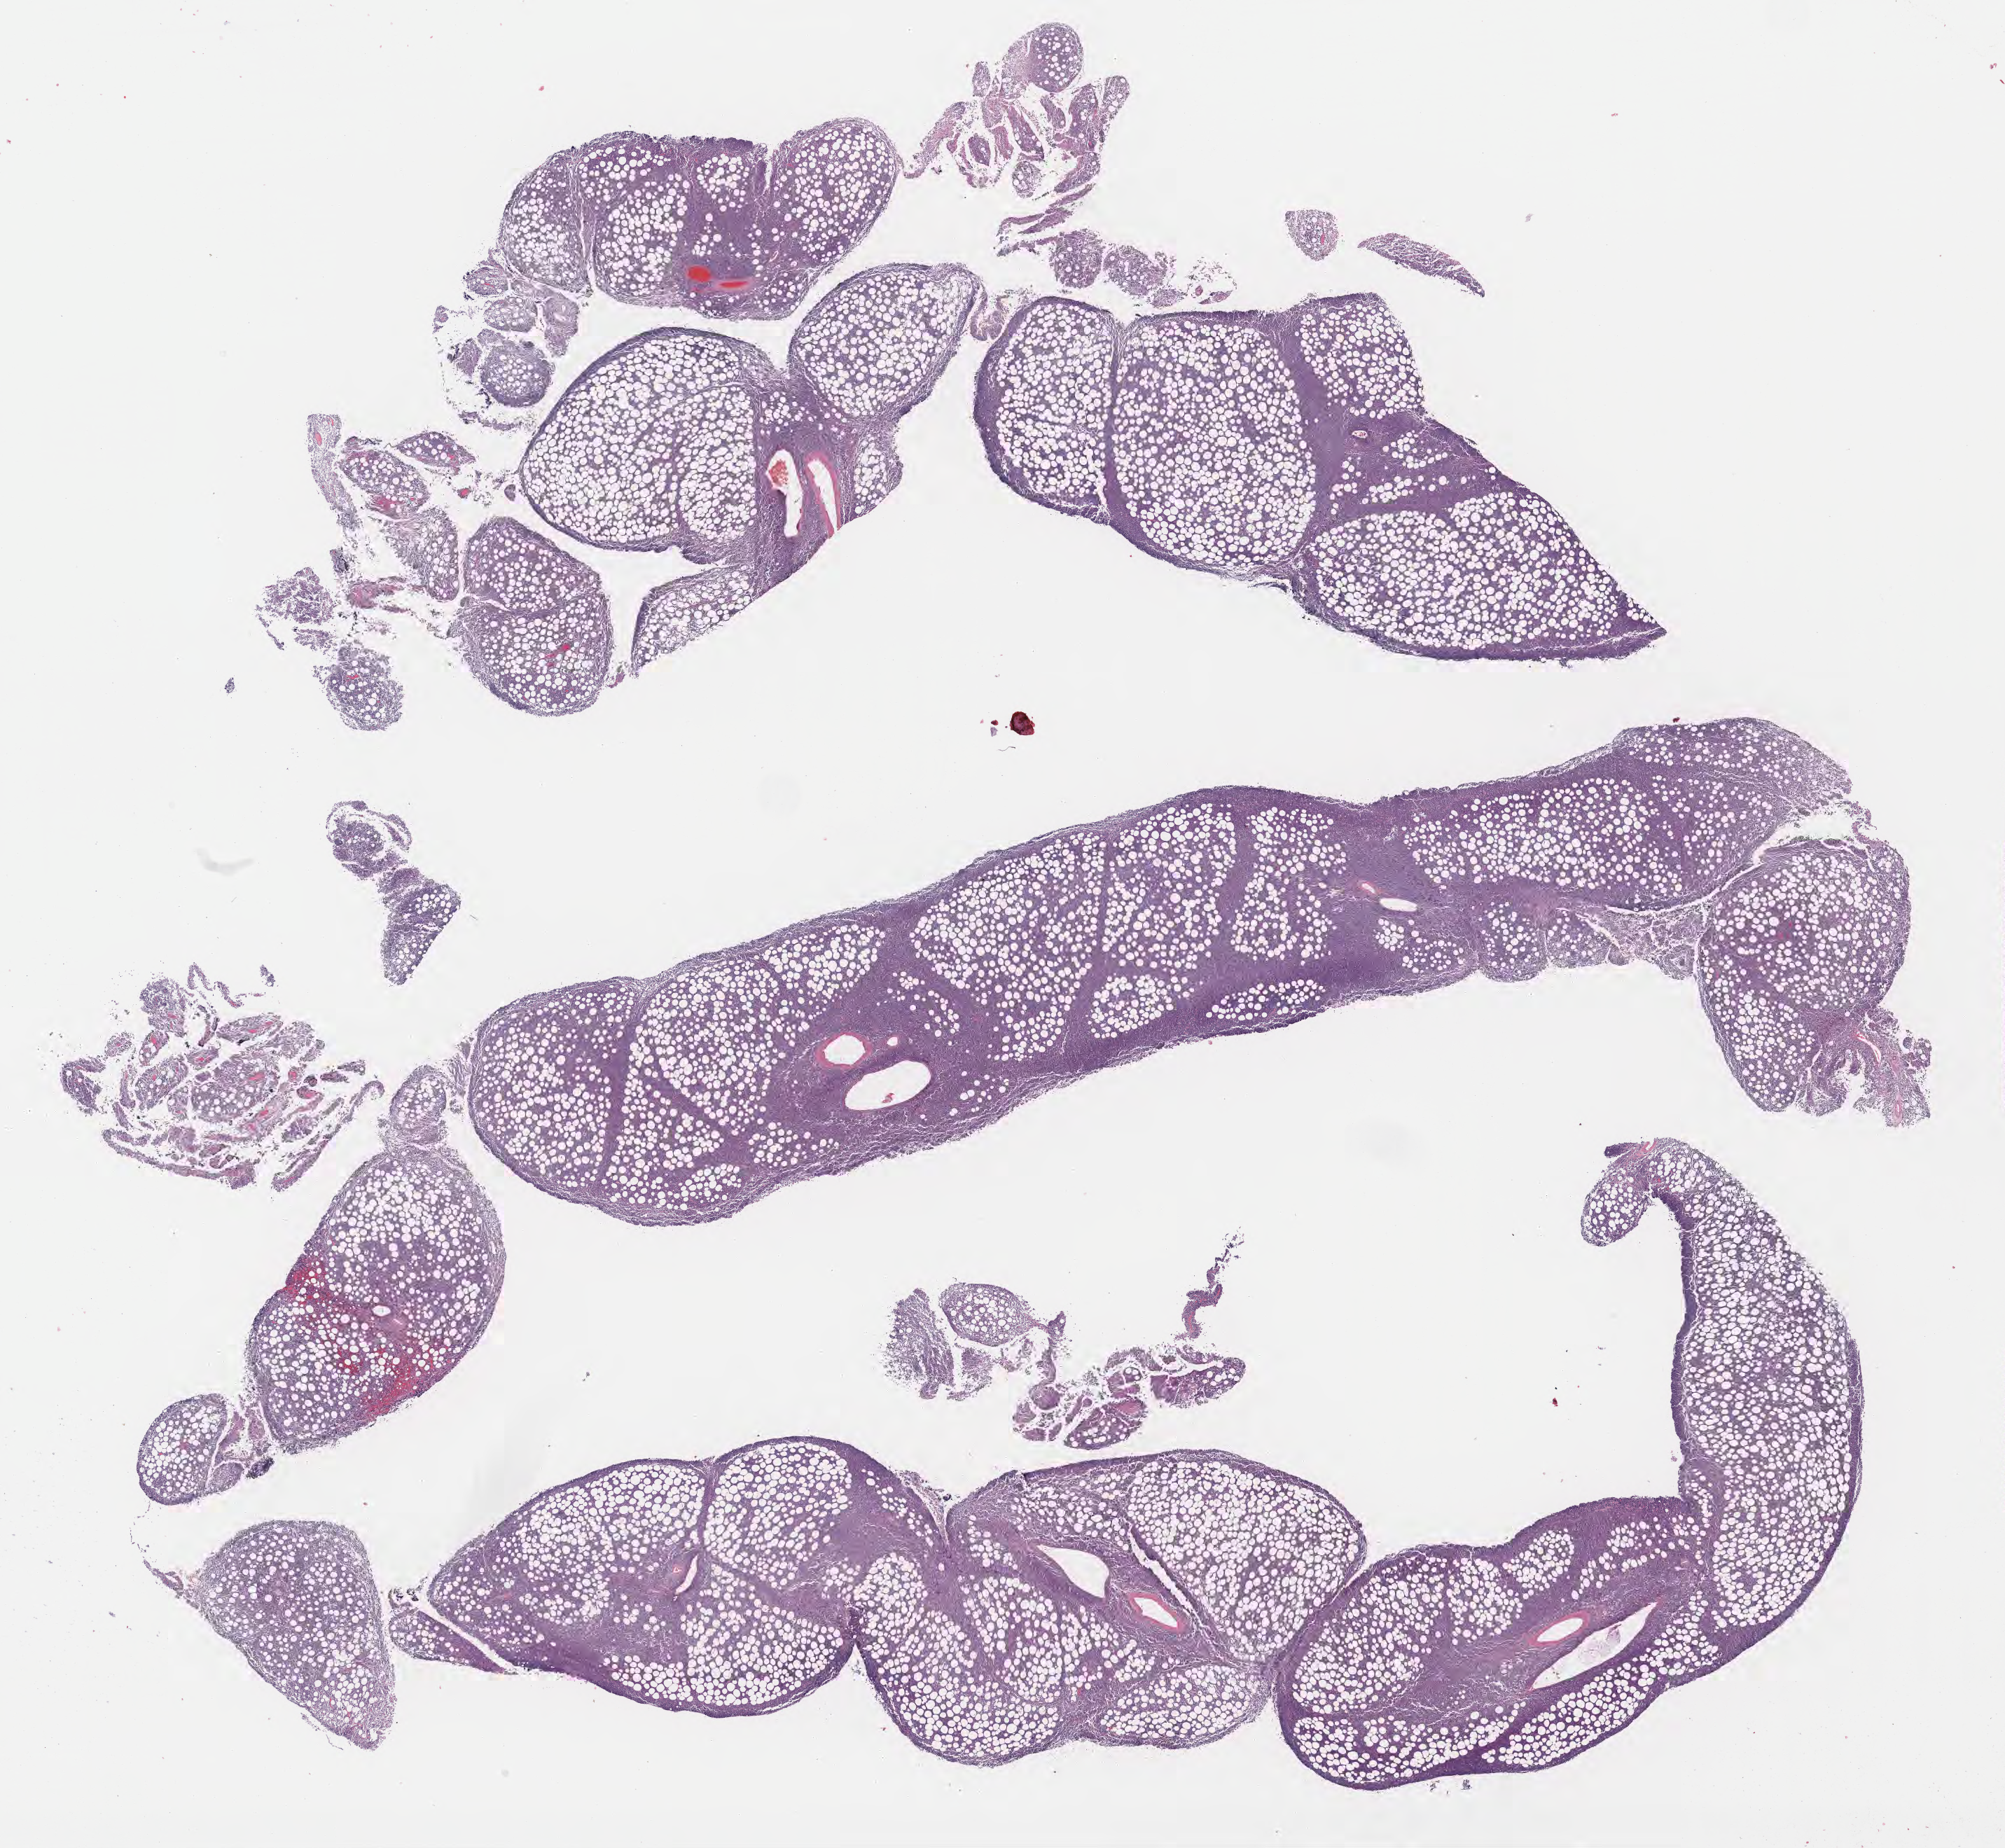
Whole-slide image, haematoxylin and eosin stain — whole scanned area (about 23.2 x 21.3 mm) shown as a low-resolution overview. Tumor tissue. Site: abdomen proper. Female patient; age at initial diagnosis 9 years.
Histologic diagnosis: Burkitt lymphoma, NOS.